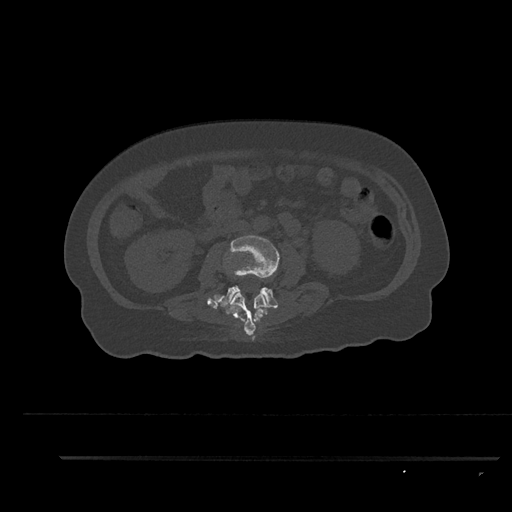
CT including the spine, one axial slice. Slice 118 of 797 in the series (ordered by position). Reconstruction kernel Br40s/3. Bone window (W 1800 / L 400 HU). 512 × 512 image matrix. Female patient, age 44 years. Case-level facts recorded for this patient, not image findings: primary cancer: renal.
Annotated regions visible in this slice (semi-automatic segmentation, software-assisted and operator-edited):
- L2 vertebra: bounding box (x1, y1, x2, y2) in pixels: (224, 293, 268, 336)
- L3 vertebra: (218, 235, 280, 308)